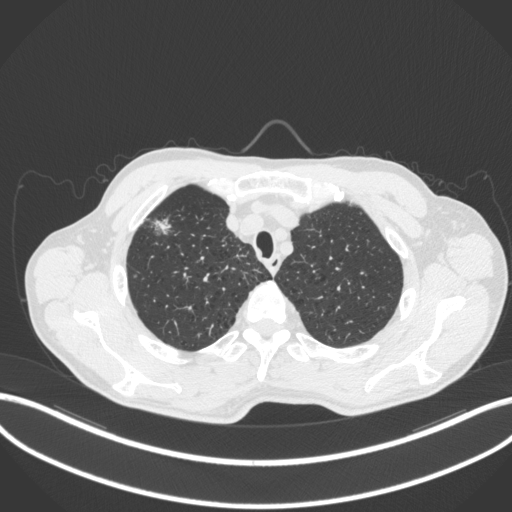
Chest CT, one axial slice. Position 356 of 414 along the scan axis. Reconstruction kernel B31f. 120 kVp. Lung window (W 1500 / L -600 HU). 1 mm slice thickness. 512 × 512 image matrix, field of view 400 × 400 mm. Patient: male, 69 years. Case-level facts recorded for this patient, not image findings: clinical TNM (as recorded): T1b N1 M0.
Annotated regions visible in this slice (bounding box drawn by a radiologist):
- lung tumour (recorded histology: adenocarcinoma): bounding box <152,210,173,237> (left, top, right, bottom; pixels)